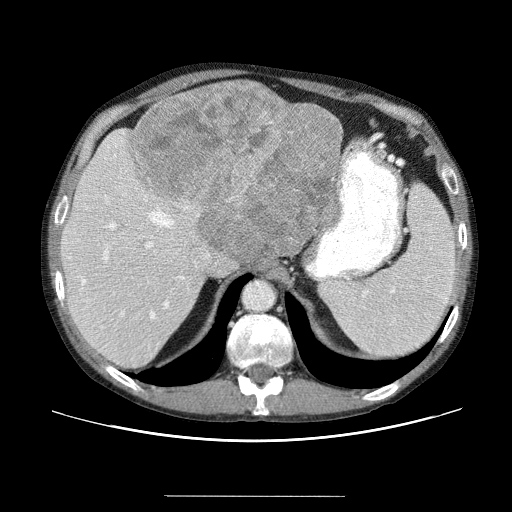
Contrast-enhanced abdominal CT (liver protocol), one axial slice. Slice 39 of 69 in the series (ordered by position). Reconstruction kernel STANDARD. 120 kVp. Soft-tissue window (W 400 / L 40 HU). 2.5 mm slice thickness. 512 × 512 image matrix, field of view 380 × 380 mm. Case-level facts recorded for this patient, not image findings: diagnosis: hepatocellular carcinoma (patient treated with transarterial chemoembolisation; whether this scan precedes or follows treatment is not stated here); TNM stage (as recorded): Stage-IVB; Child-Pugh class: B; tumour differentiation: poorly differentiated.
Structures marked on this image (semi-automatic segmentation, software-assisted and operator-edited):
- liver parenchyma outside the tumour (the mass and vessels are separate outlines, so this box may not span the whole liver): bounding box (x1, y1, x2, y2) in pixels: (60, 94, 340, 370)
- mass: (131, 80, 343, 259)
- liver vessels: (91, 145, 177, 348)